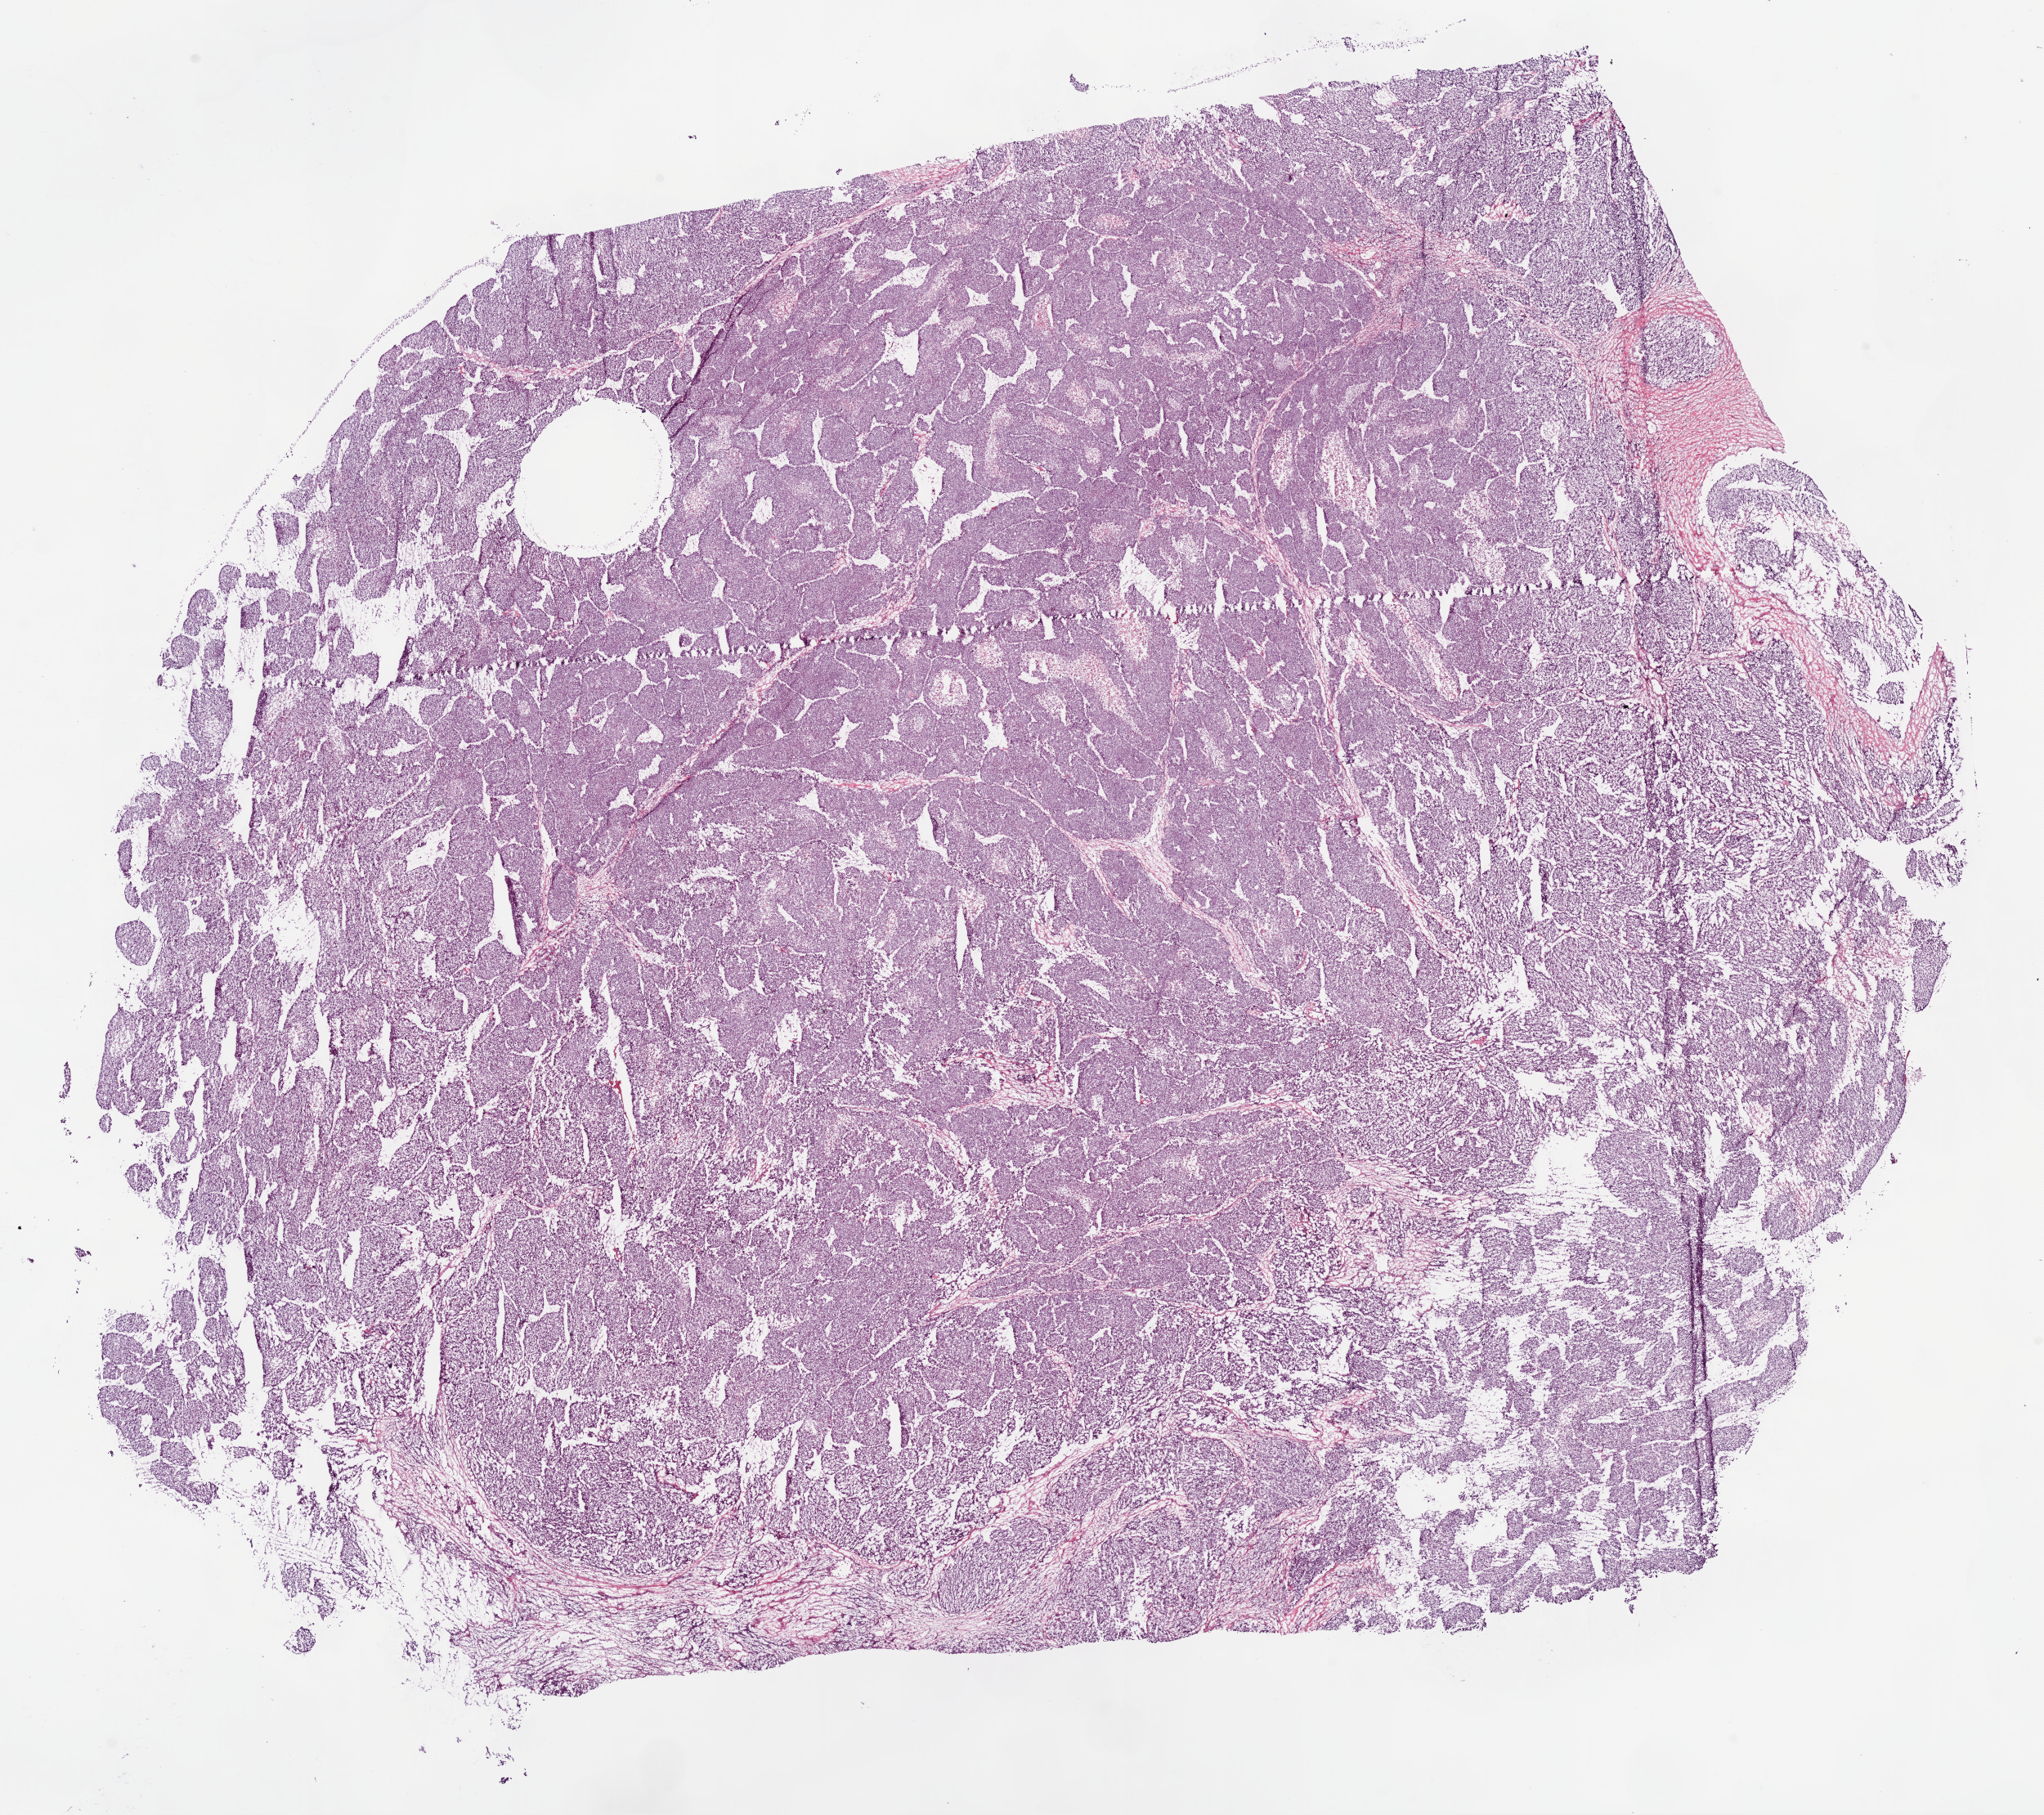
Digitized H&E-stained tissue section (whole slide), shown as a low-resolution overview of the whole scanned area (about 20.1 x 17.8 mm); frozen section from the bottom of the tissue portion; primary tumour sample from the liver. Male patient; age at initial diagnosis 71 years. Histologic grade: G2 (moderately differentiated). Composition of this section per pathologist review: tumour cells 90%, tumour nuclei 85%, normal cells 0%, stromal cells 5%, necrosis 5%.
* pathologic diagnosis: Hepatocellular carcinoma, NOS
* AJCC pathologic stage: IIIA (6th edition)